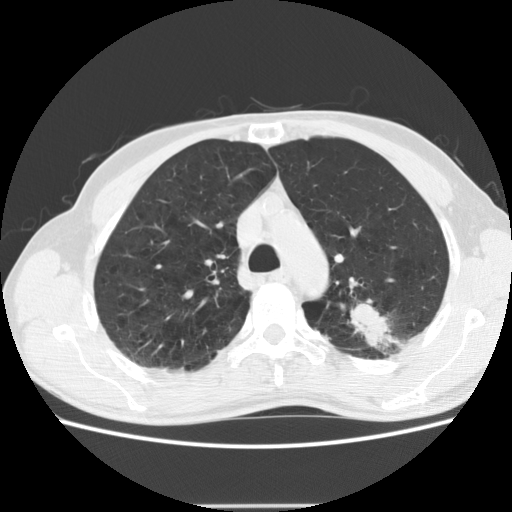
Low-dose screening chest CT, one axial slice; position 144 of 191 along the scan axis; 120 kVp; lung window (W 1500 / L -600 HU); 2.5 mm slice thickness; 512 × 512 image matrix, field of view 352 × 352 mm.
Annotated regions visible in this slice (expert manual segmentation):
- lesion 1 (tumor, upper lobe of left lung): bounding box <350,302,390,346> (left, top, right, bottom; pixels)